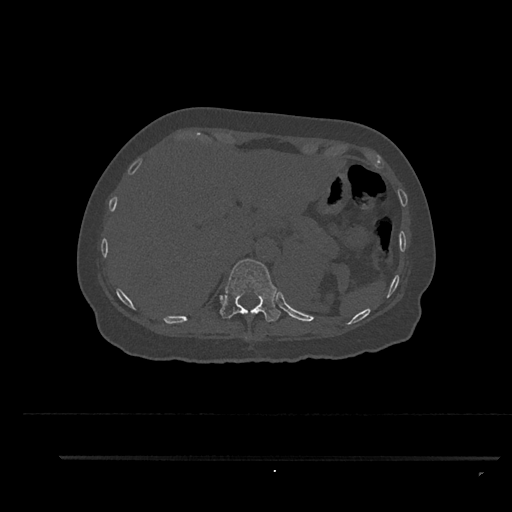
CT including the spine, one axial slice; position 323 of 797 along the scan axis; bone window (W 1800 / L 400 HU); 512 × 512 image matrix, field of view 408 × 408 mm. Patient: female, 44 years. From the clinical record (not read from this slice): primary cancer: renal.
Structures marked on this image (semi-automatically segmented with operator editing):
- T11 vertebra: bounding box [x1, y1, x2, y2] px = [220, 259, 281, 322]